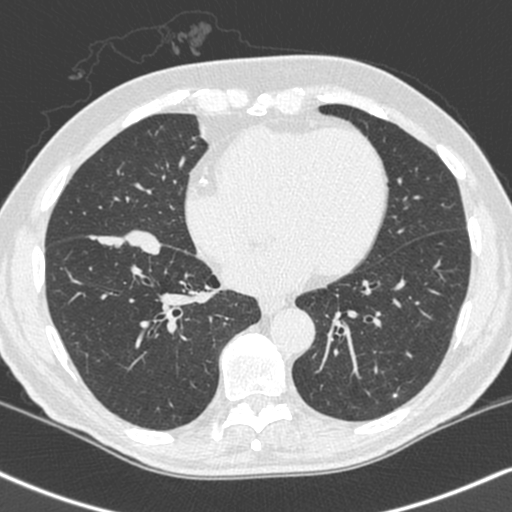
Low-dose screening chest CT, axial slice; first (baseline) screen; lung window (W 1500 / L -600 HU); 1.3 mm slice thickness; slice 142 of 248 in the series. Male participant, aged 68 years at enrolment.
Expert reader's lesion annotation, box from (x=88, y=226) to (x=163, y=297) px. The exam's reader record, not a measurement of the box and not confirmed to be the same lesion: non-calcified nodule or mass ≥4 mm, right lower lobe, 34 × 17 mm, smooth margins, soft tissue attenuation. Official screen result: positive, change unspecified: nodule(s) >= 4 mm or enlarging nodule(s), mass(es), or other non-specific abnormalities suspicious for lung cancer. Lung cancer was diagnosed 24 days after this screen: combined small cell carcinoma, right lower lobe, stage IIIA (AJCC 6th edition), 41 mm at pathology.